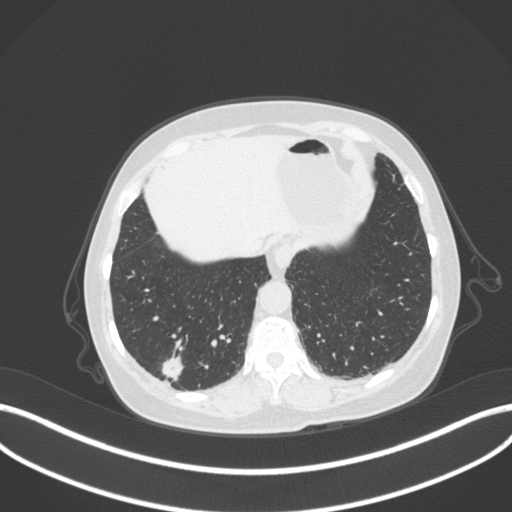
Chest CT, one axial slice. Slice 58 of 340 in the series (ordered by position). 120 kVp. Lung window (W 1500 / L -600 HU). 1 mm slice thickness. 512 × 512 image matrix, field of view 400 × 400 mm. Female patient, age 69 years. Case-level facts recorded for this patient, not image findings: clinical TNM (as recorded): T1b N0 M0; histopathological grade: G2-3.
Outlined on this slice (rectangle marked by the reading radiologist):
- lung tumour (recorded histology: adenocarcinoma): bounding box [x1, y1, x2, y2] px = [158, 349, 186, 381]